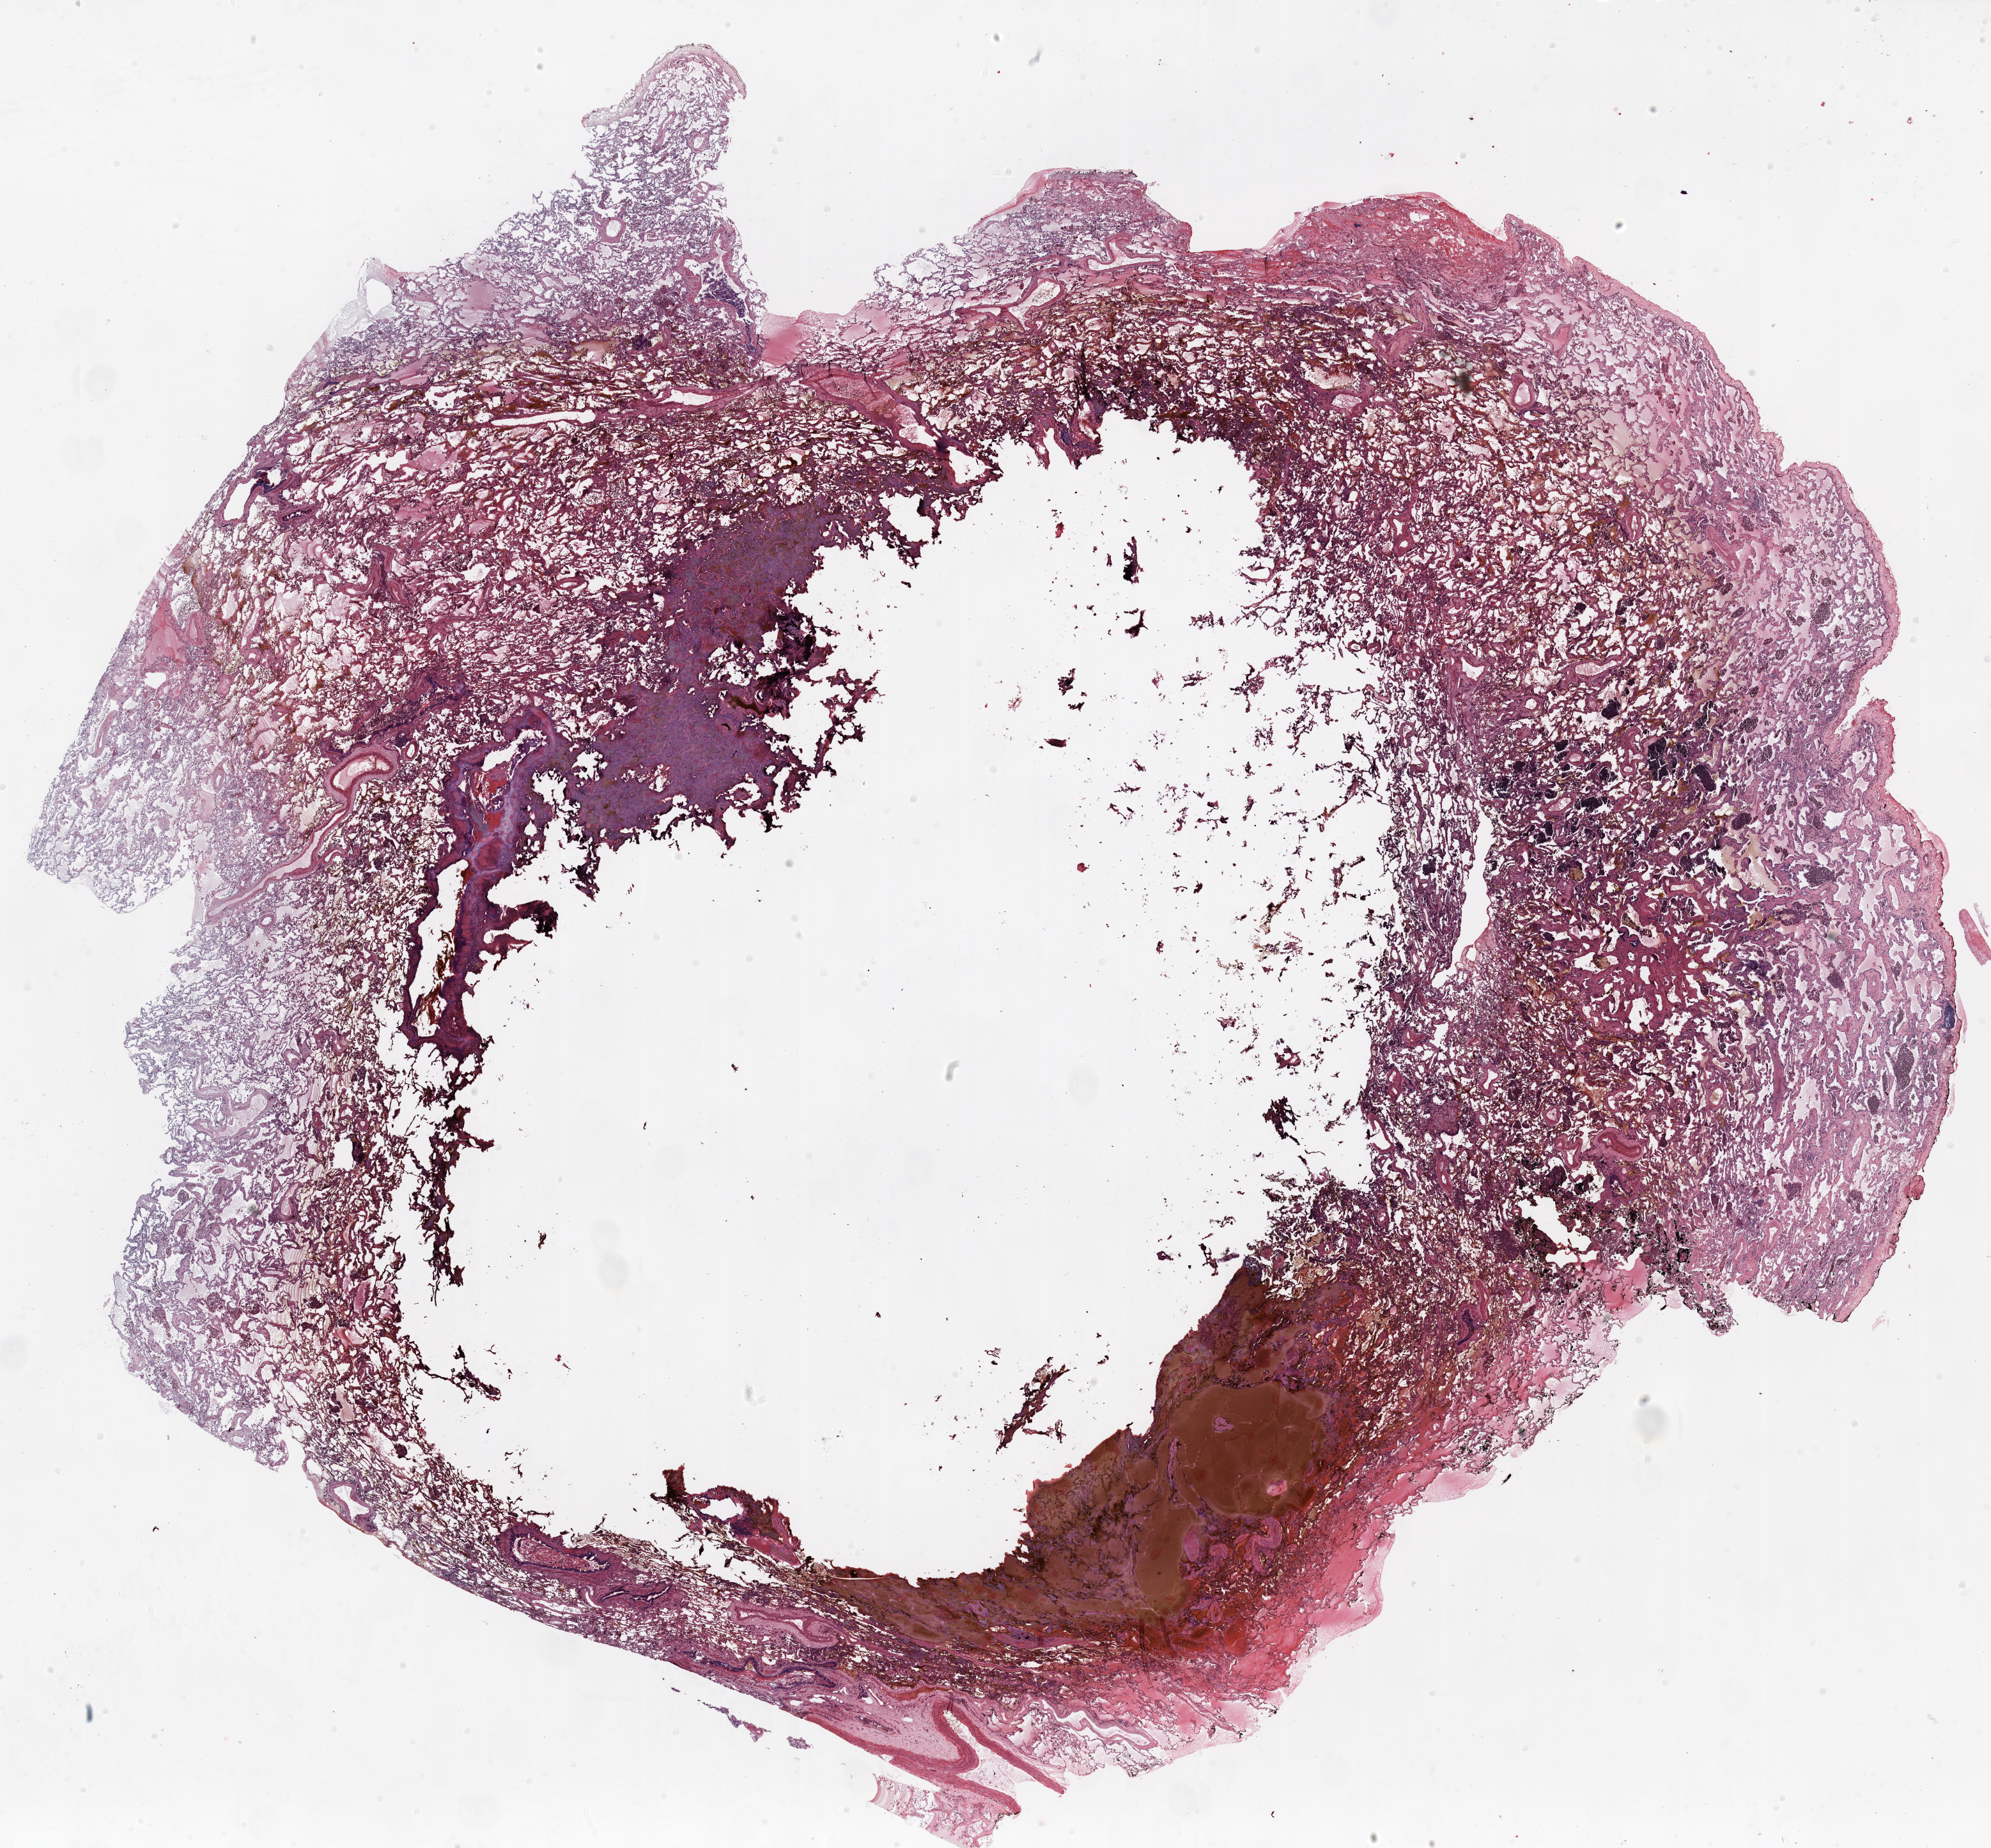
Whole-slide histology image, H&E-stained — shown as a low-resolution overview of the whole scanned area (about 25.0 x 23.2 mm, acquisition: 20x scan); FFPE section; lung. Female, age 60 at enrolment. Current smoker at enrolment.
Participant's lung-cancer diagnosis: Squamous cell carcinoma, keratinizing, NOS. Note: participant had 2 primary lung cancers recorded; fields above describe the first.